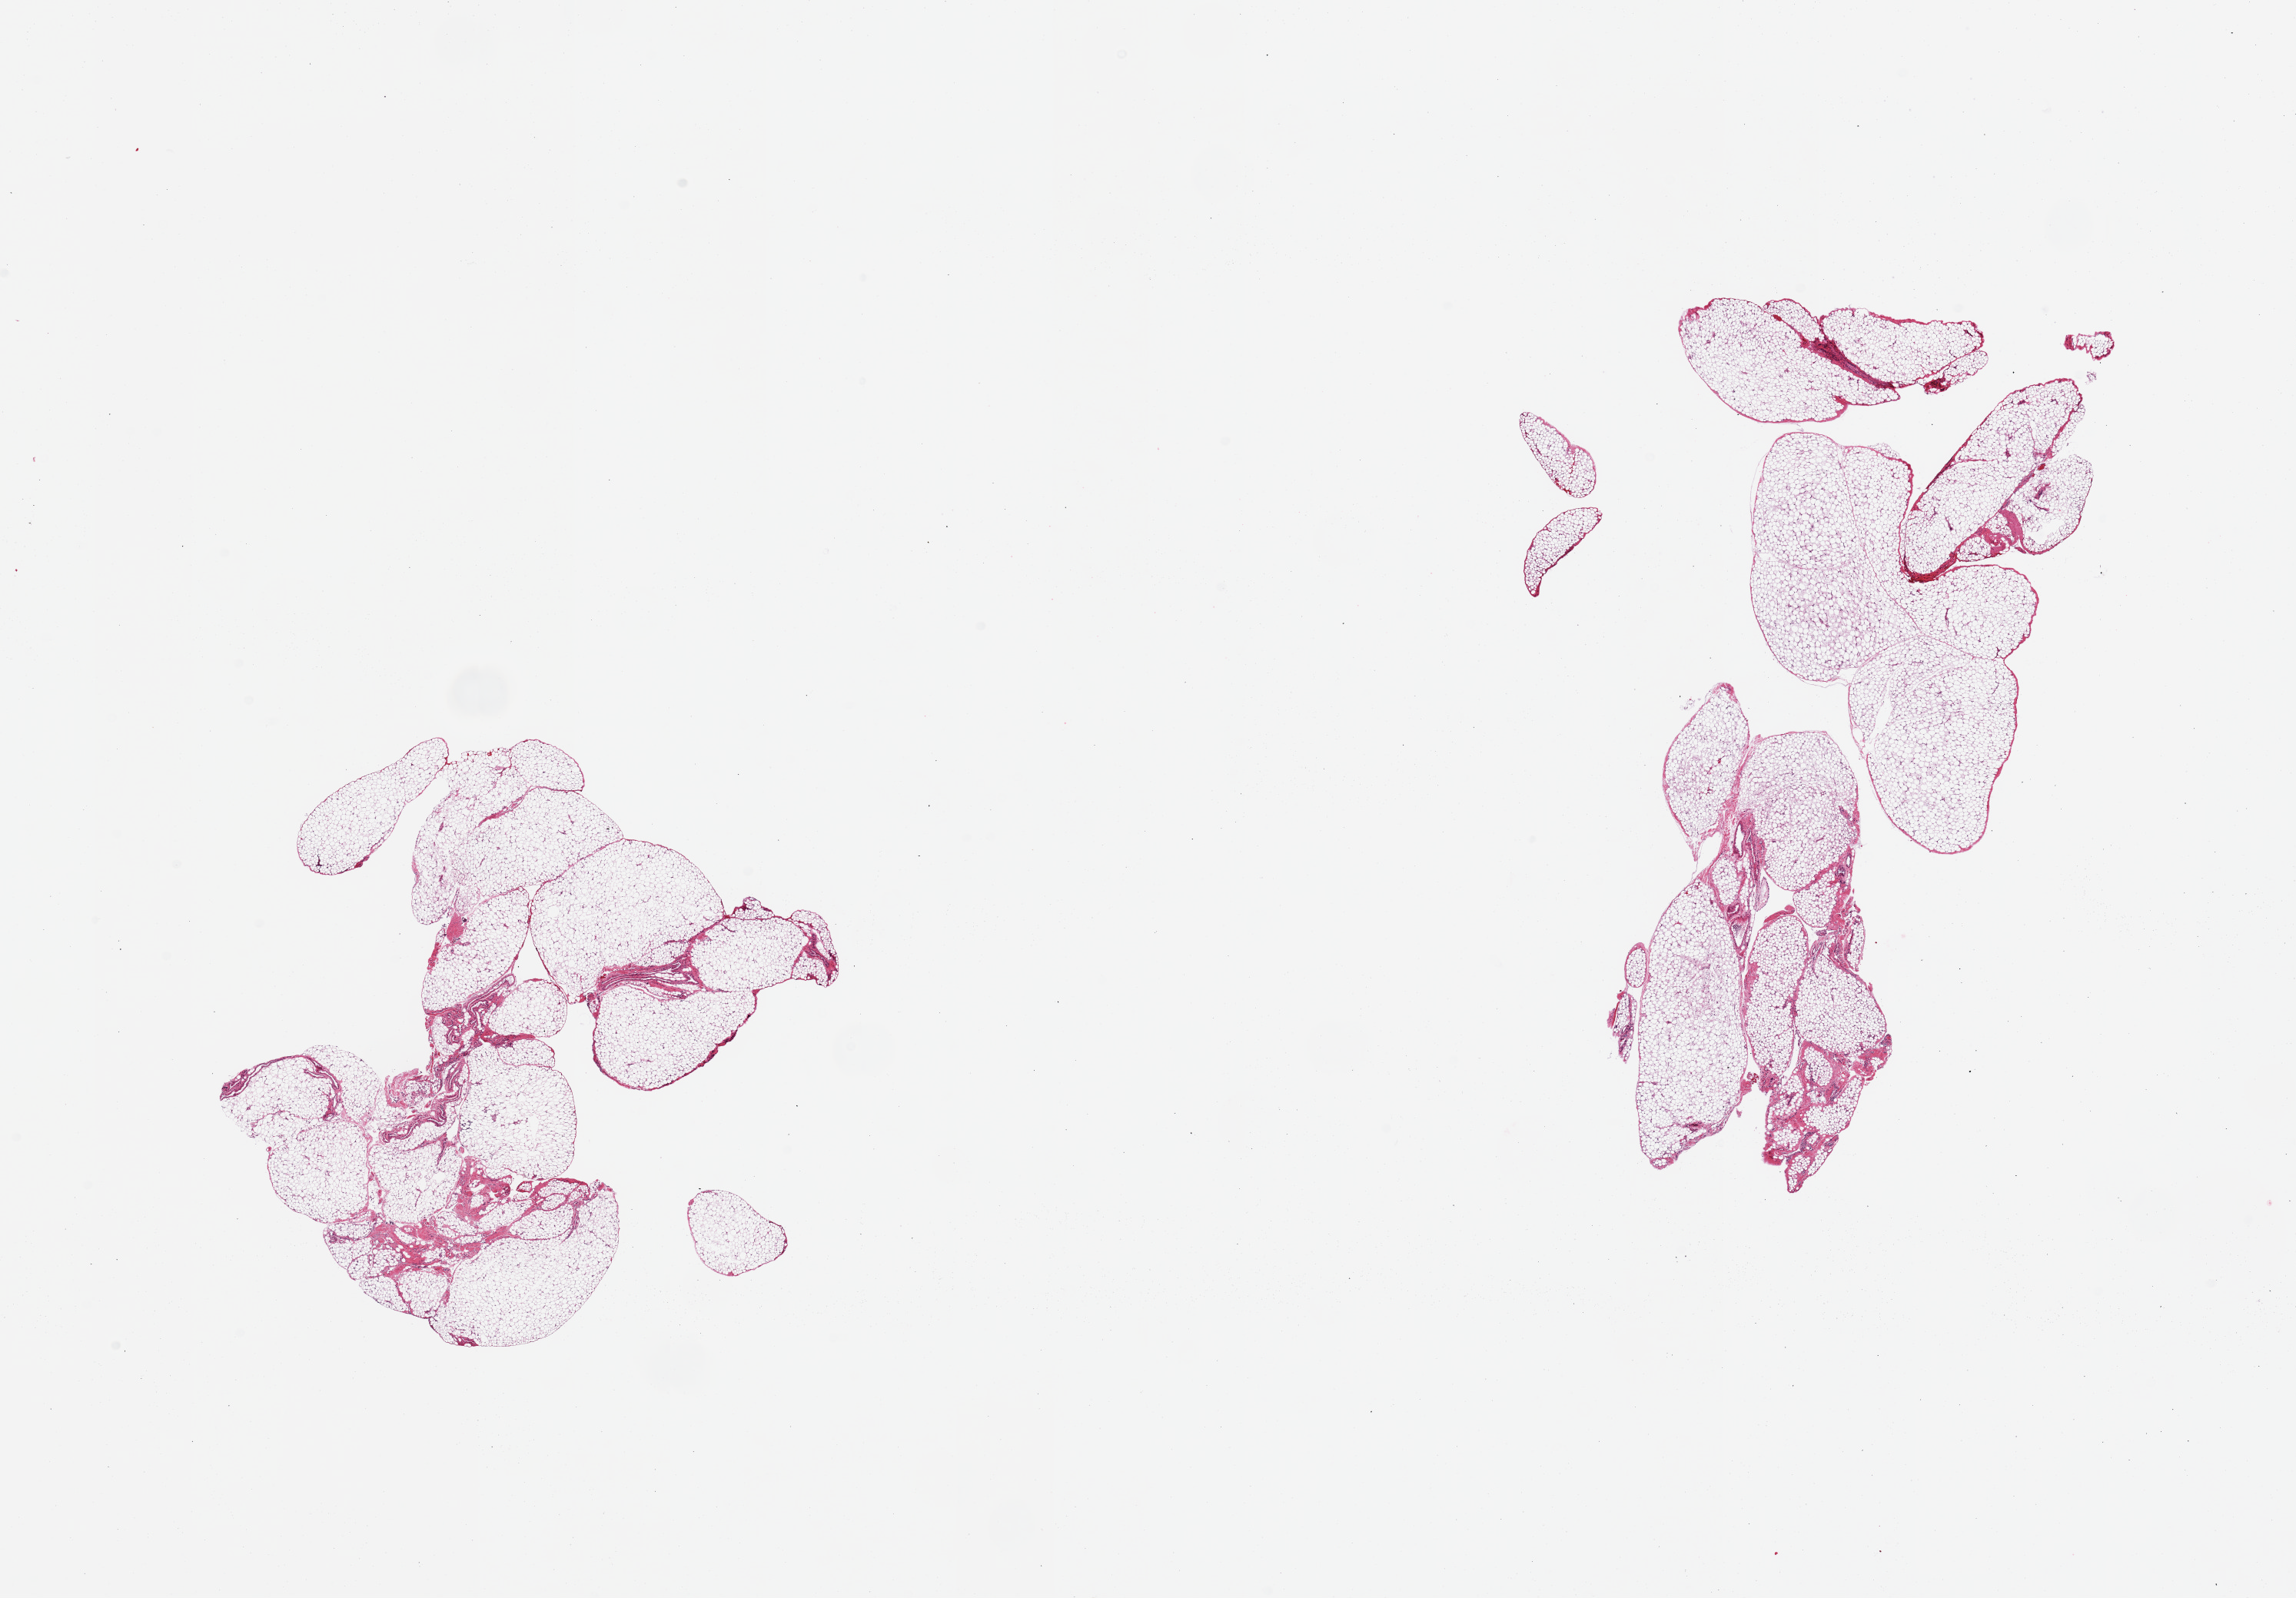
Haematoxylin and eosin whole-slide image, whole scanned area (about 23.6 x 16.4 mm, slide scanned at 20x) shown as a low-resolution overview. PAXgene-fixed, paraffin-embedded tissue. Target tissue: omentum. Donor tissue sample. Donor sex: female.
Reviewer comment on this tissue sample: 2 pieces, ~5-10% mesothelial/fascia hyerplasia, interstitial.